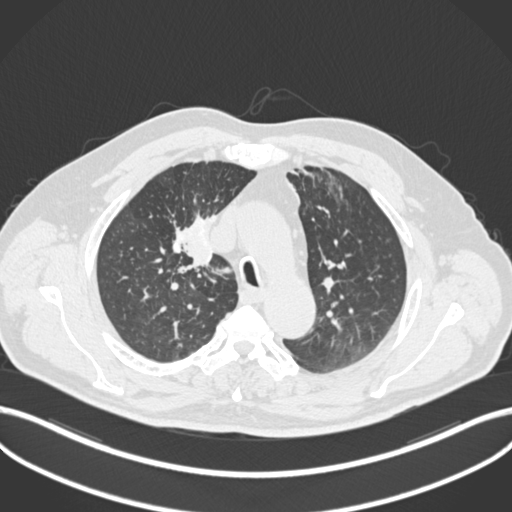
Chest CT, one axial slice; position 144 of 255 along the scan axis; 120 kVp; lung window (W 1500 / L -600 HU); 1 mm slice thickness; 512 × 512 image matrix, field of view 400 × 400 mm. Patient: male, 60 years. Case-level facts recorded for this patient, not image findings: clinical TNM (as recorded): T1b N1 M0.
Outlined on this slice (rectangle marked by the reading radiologist):
- lung tumour (recorded histology: squamous cell carcinoma): bounding box <168,211,221,277> (left, top, right, bottom; pixels)